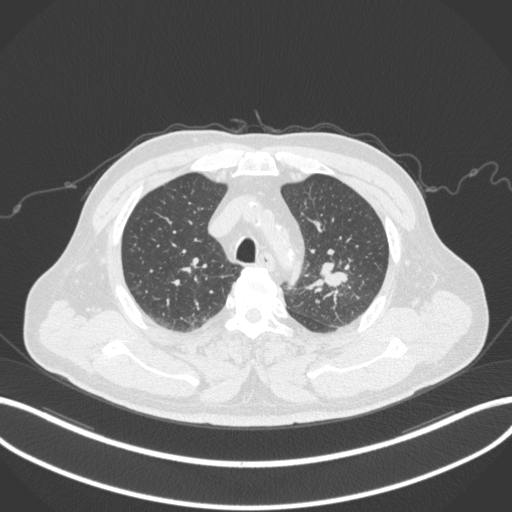
Chest CT, one axial slice. Slice 235 of 286 in the series (ordered by position). 120 kVp. Lung window (W 1500 / L -600 HU). 1 mm slice thickness. 512 × 512 image matrix, field of view 400 × 400 mm. Male patient, age 67 years. From the clinical record (not read from this slice): clinical TNM (as recorded): T2a N1 M0.
Structures marked on this image (bounding box drawn by a radiologist):
- lung tumour (recorded histology: adenocarcinoma): bounding box (x1, y1, x2, y2) in pixels: (316, 257, 349, 292)